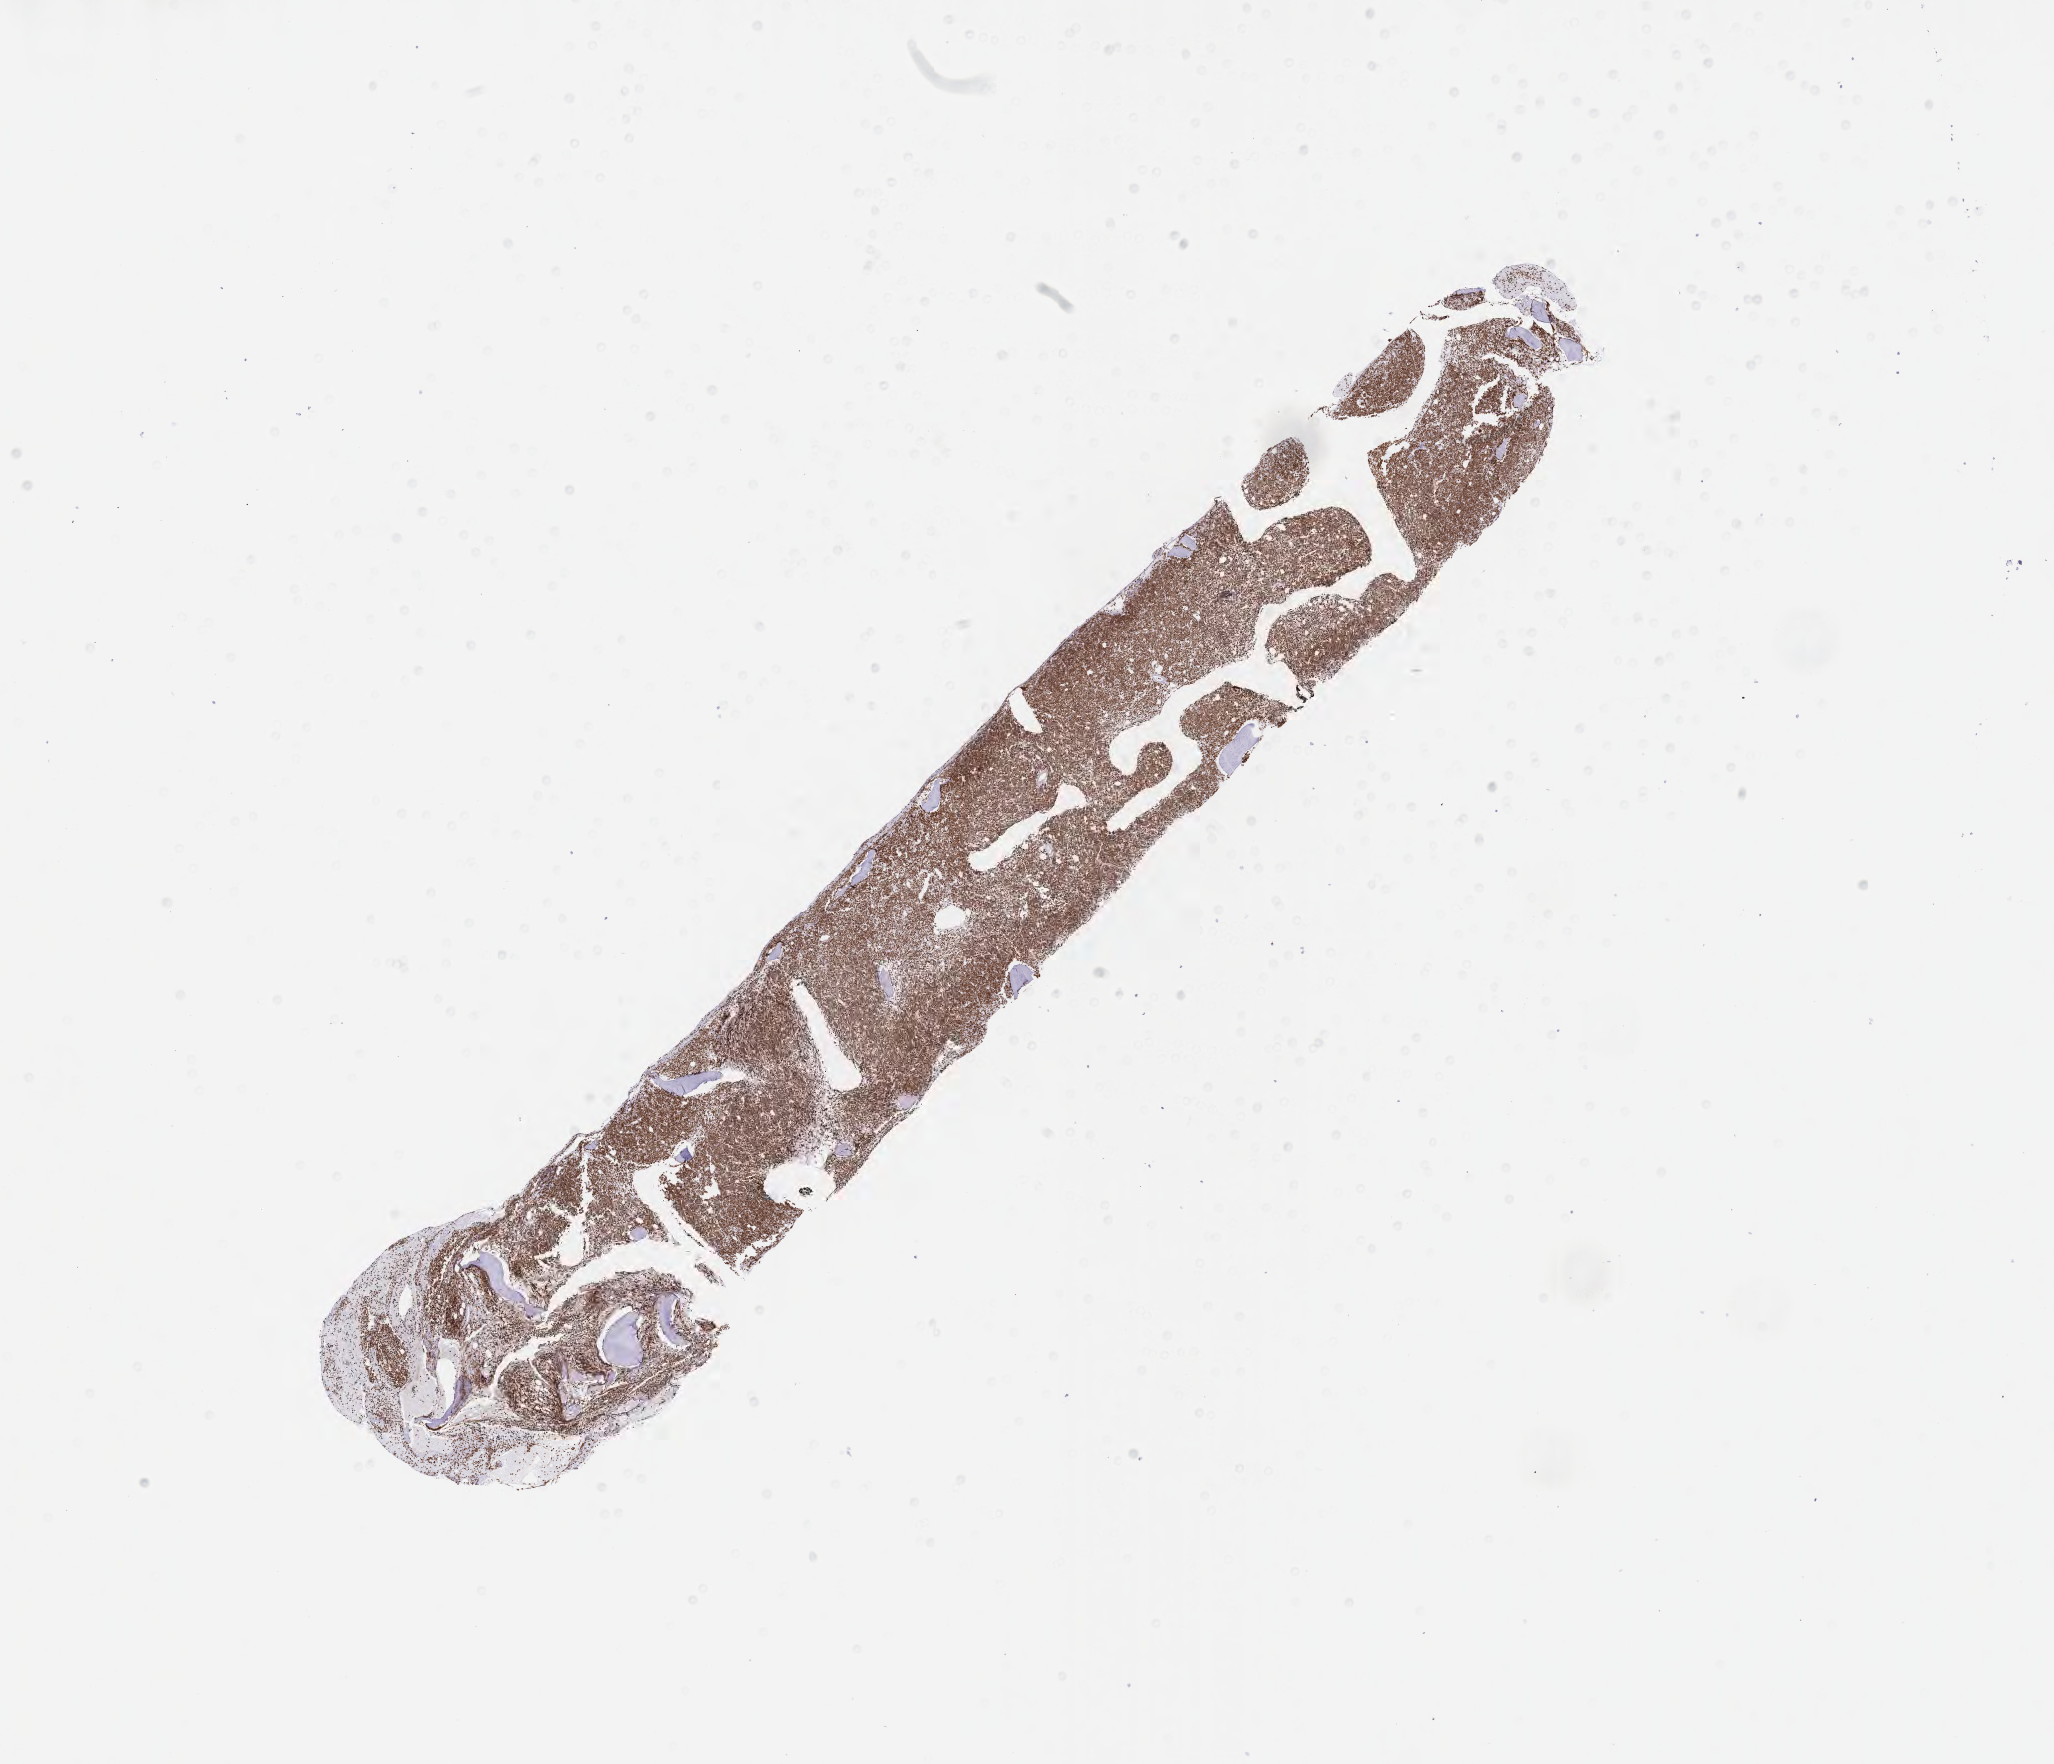
IHC for Ki-67, whole-slide image — whole scanned area (about 16.6 x 14.3 mm) shown as a low-resolution overview; specimen: tumor tissue. Female patient, aged 64.
Diagnosis: Burkitt lymphoma, NOS.